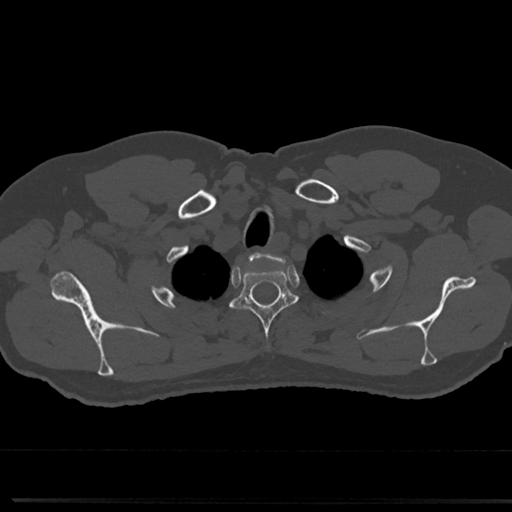
CT including the spine, one axial slice. Position 636 of 817 along the scan axis. Reconstruction kernel Br40s/3. 120 kVp. Bone window (W 1800 / L 400 HU). 0.5 mm slice thickness. 512 × 512 image matrix. Male patient, age 61 years. From the clinical record (not read from this slice): primary cancer: prostate.
Structures marked on this image (semi-automatic segmentation, software-assisted and operator-edited):
- T2 vertebra: box from (x=233, y=262) to (x=295, y=354) px
- T3 vertebra: (x=302, y=313)–(x=310, y=322)